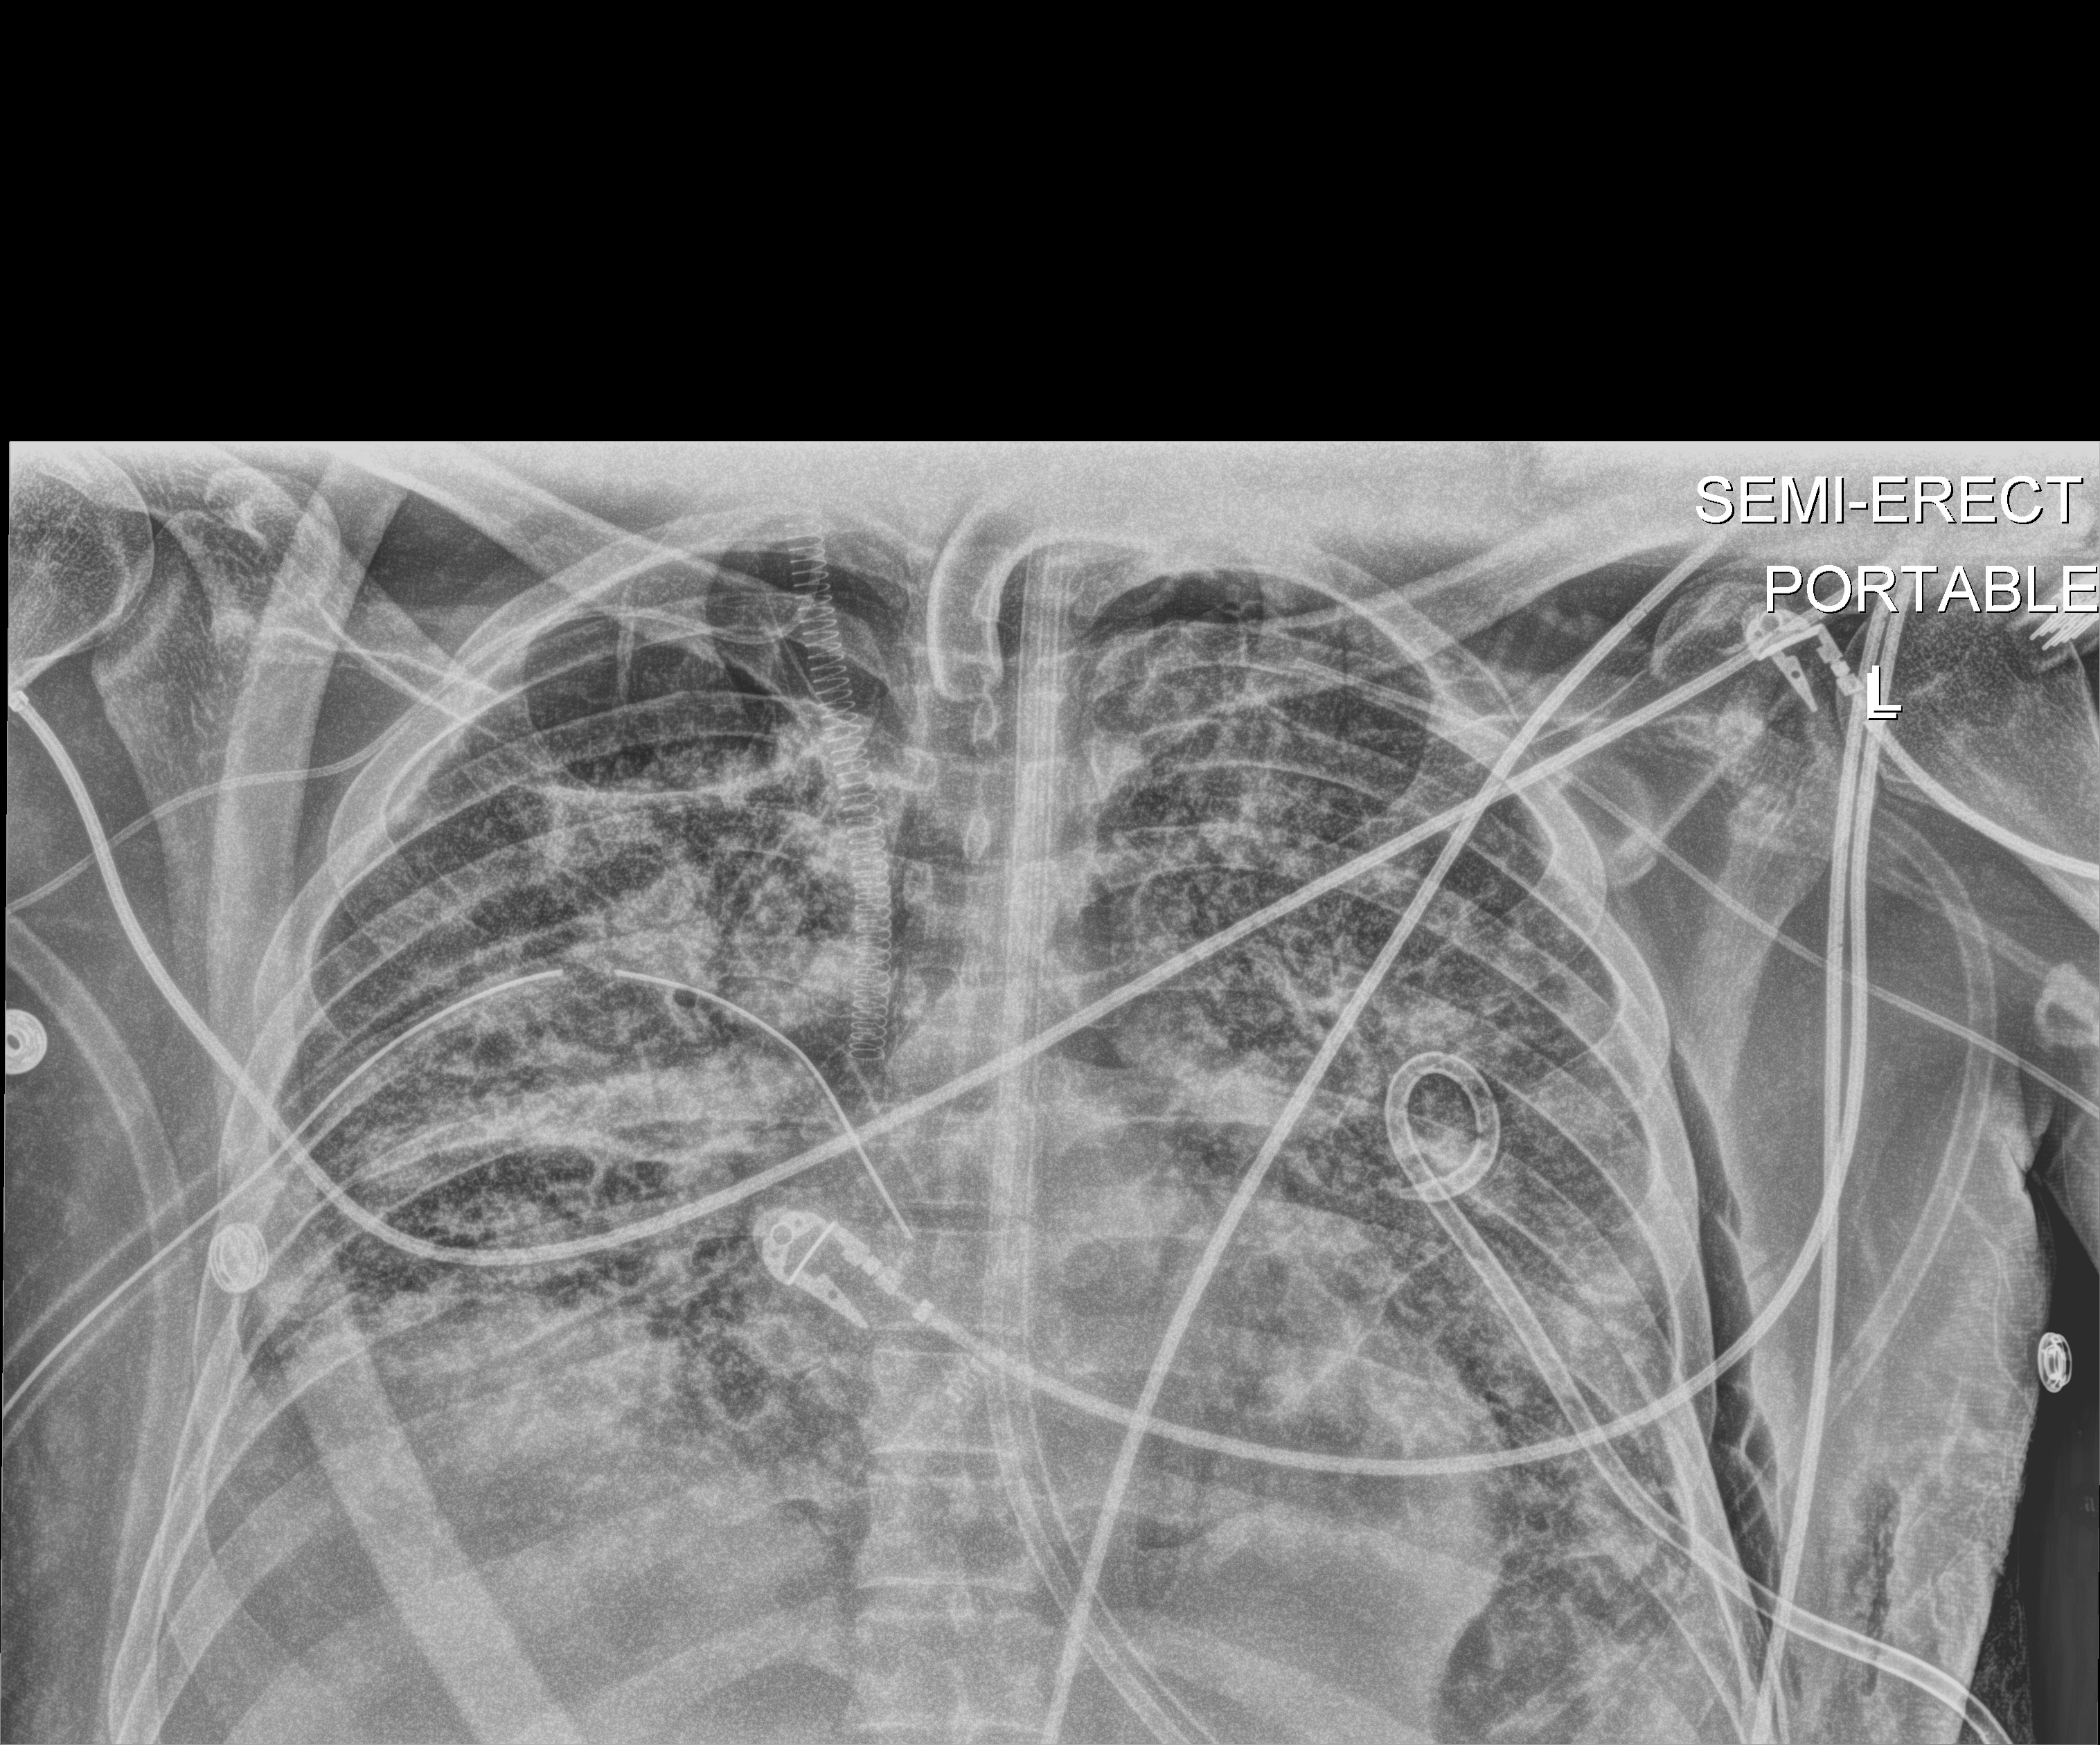
Chest X-ray (portable); anteroposterior (AP) projection. Adult patient hospitalised with COVID-19, age 18–59 years.
From the hospital-stay record, not from the radiograph (when in the stay this image was taken is not recorded): mechanically ventilated during this hospital stay: yes; admitted to intensive care during this hospital stay: yes.